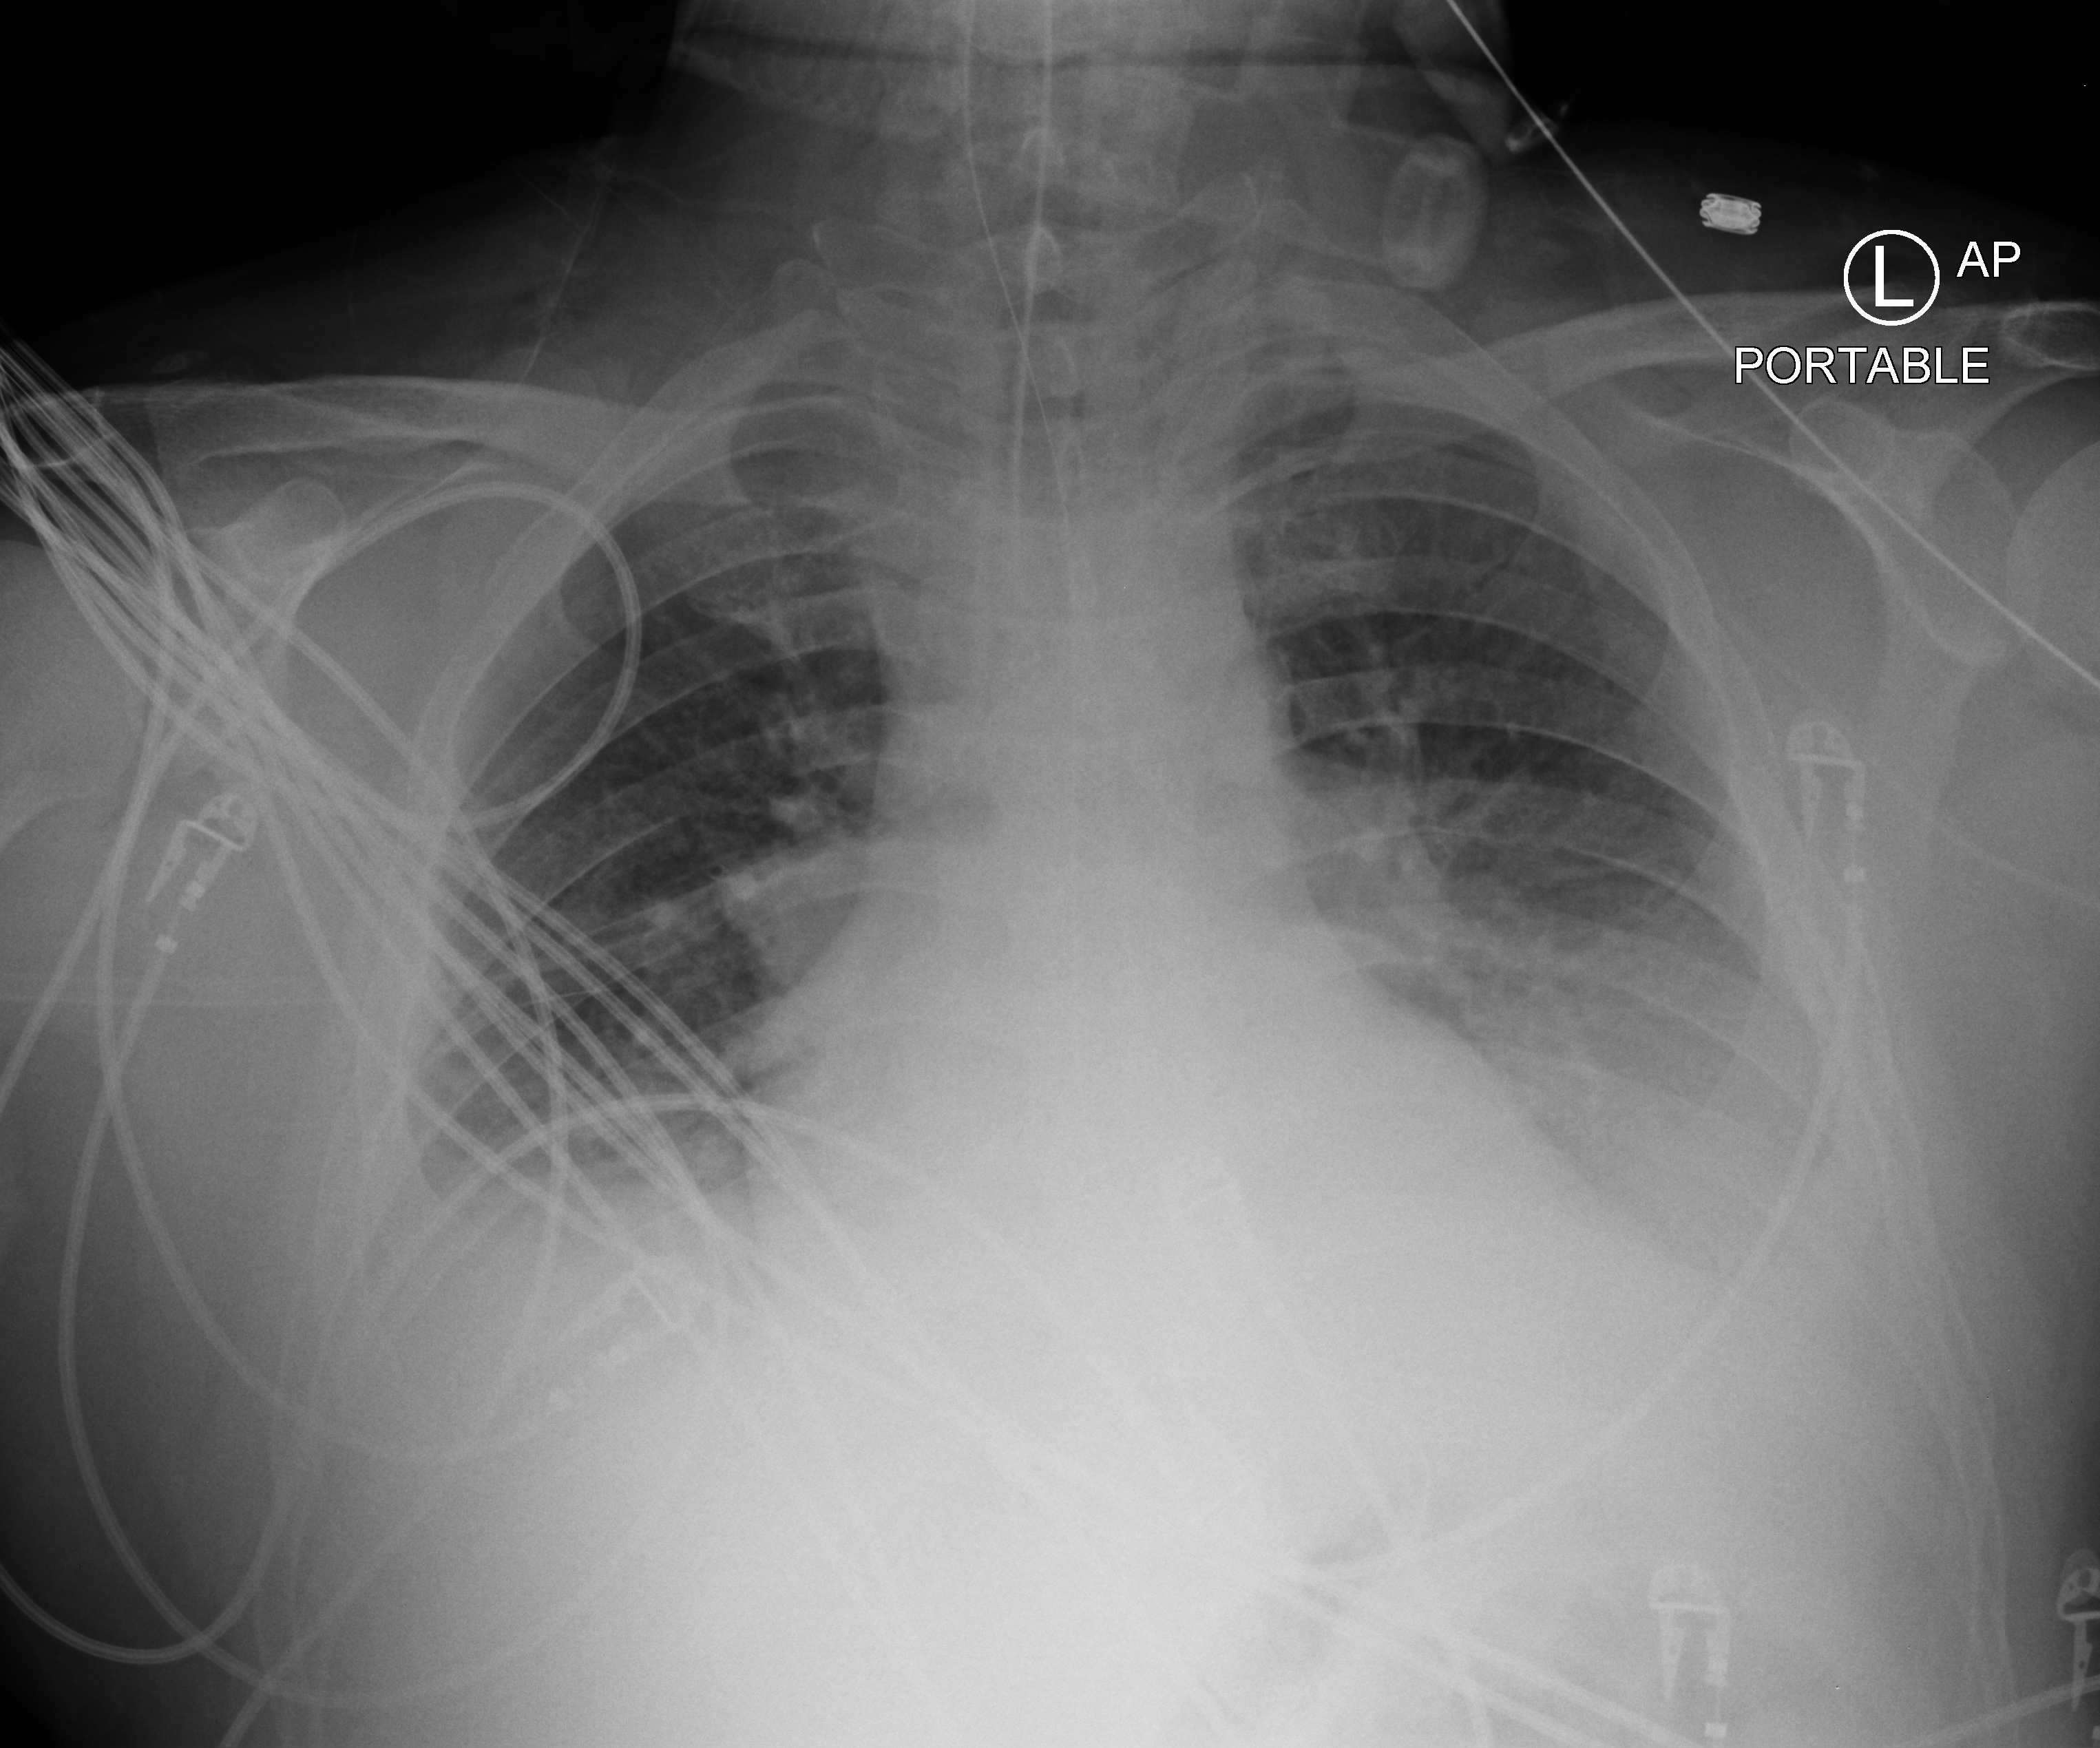
Bedside chest radiograph (computed radiography), anteroposterior (AP) projection. Male patient hospitalised with COVID-19, age 18–59 years.
Hospital-stay facts (about this admission, not read from this image; timing relative to this image not recorded): admitted to intensive care during this hospital stay: yes.